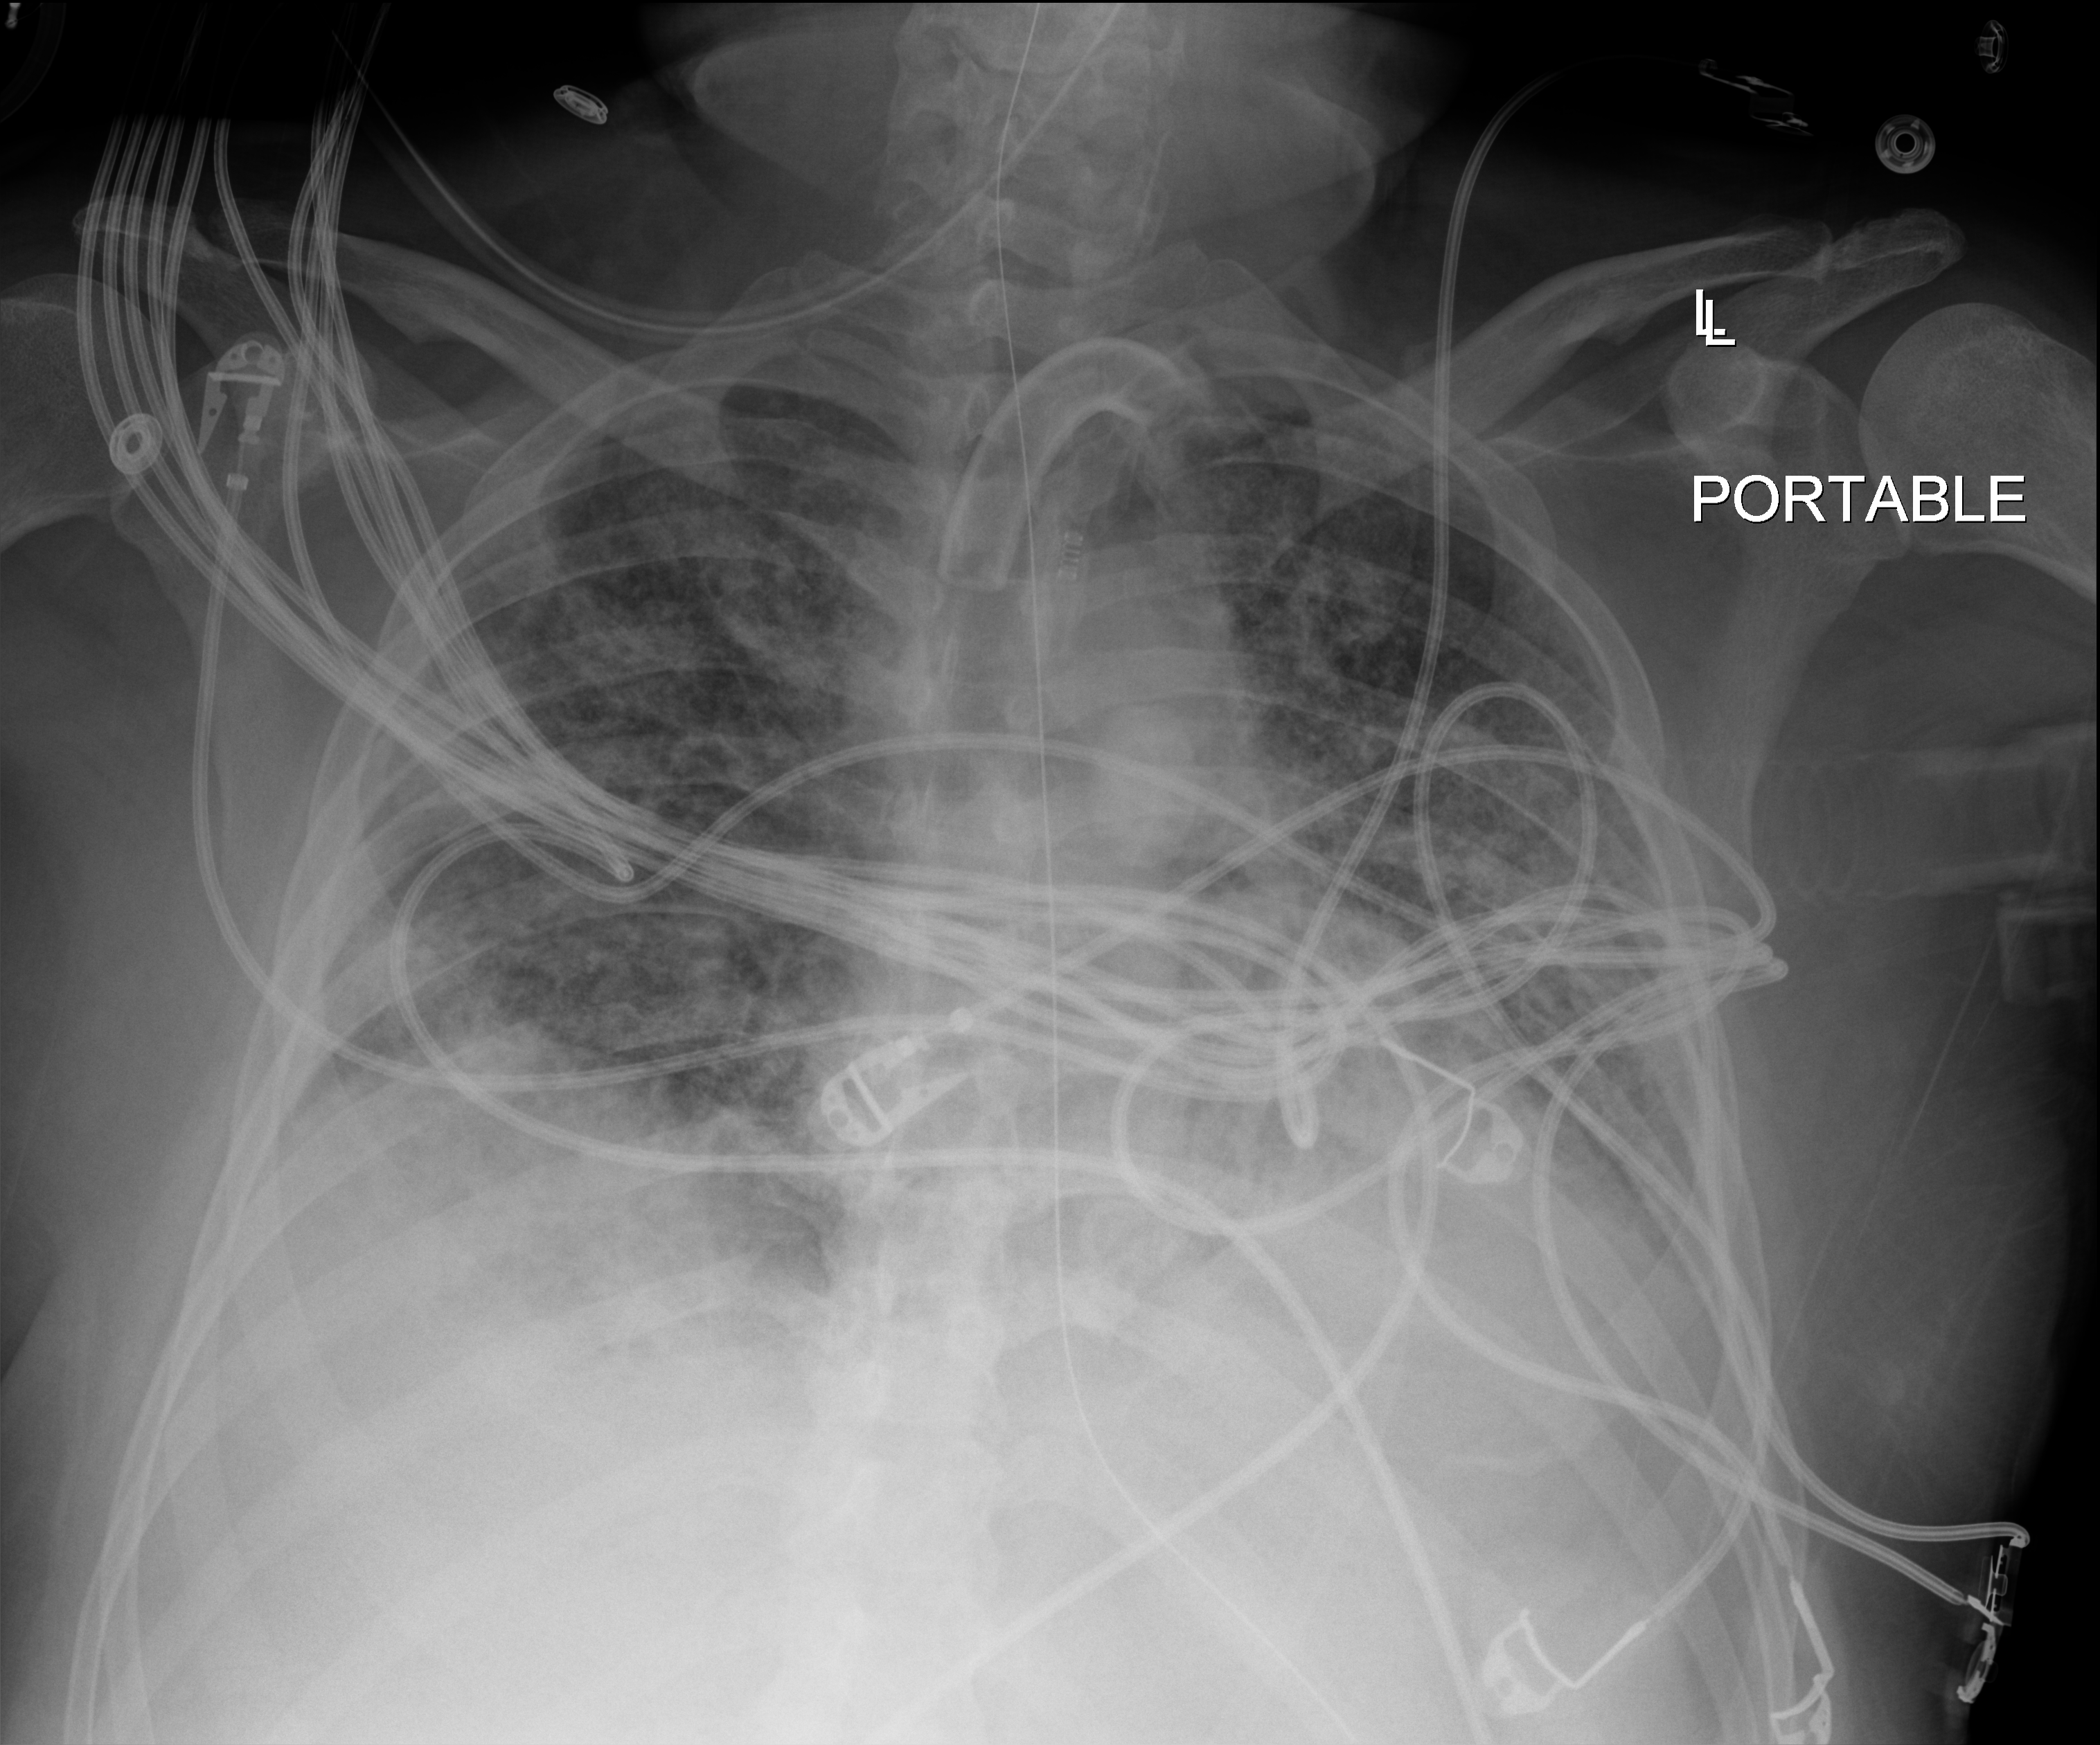
Portable chest radiograph, anteroposterior (AP) projection. Patient hospitalised with COVID-19; male, aged 18–59 years.
Hospital-stay facts (about this admission, not read from this image; timing relative to this image not recorded): admitted to intensive care during this hospital stay: yes.